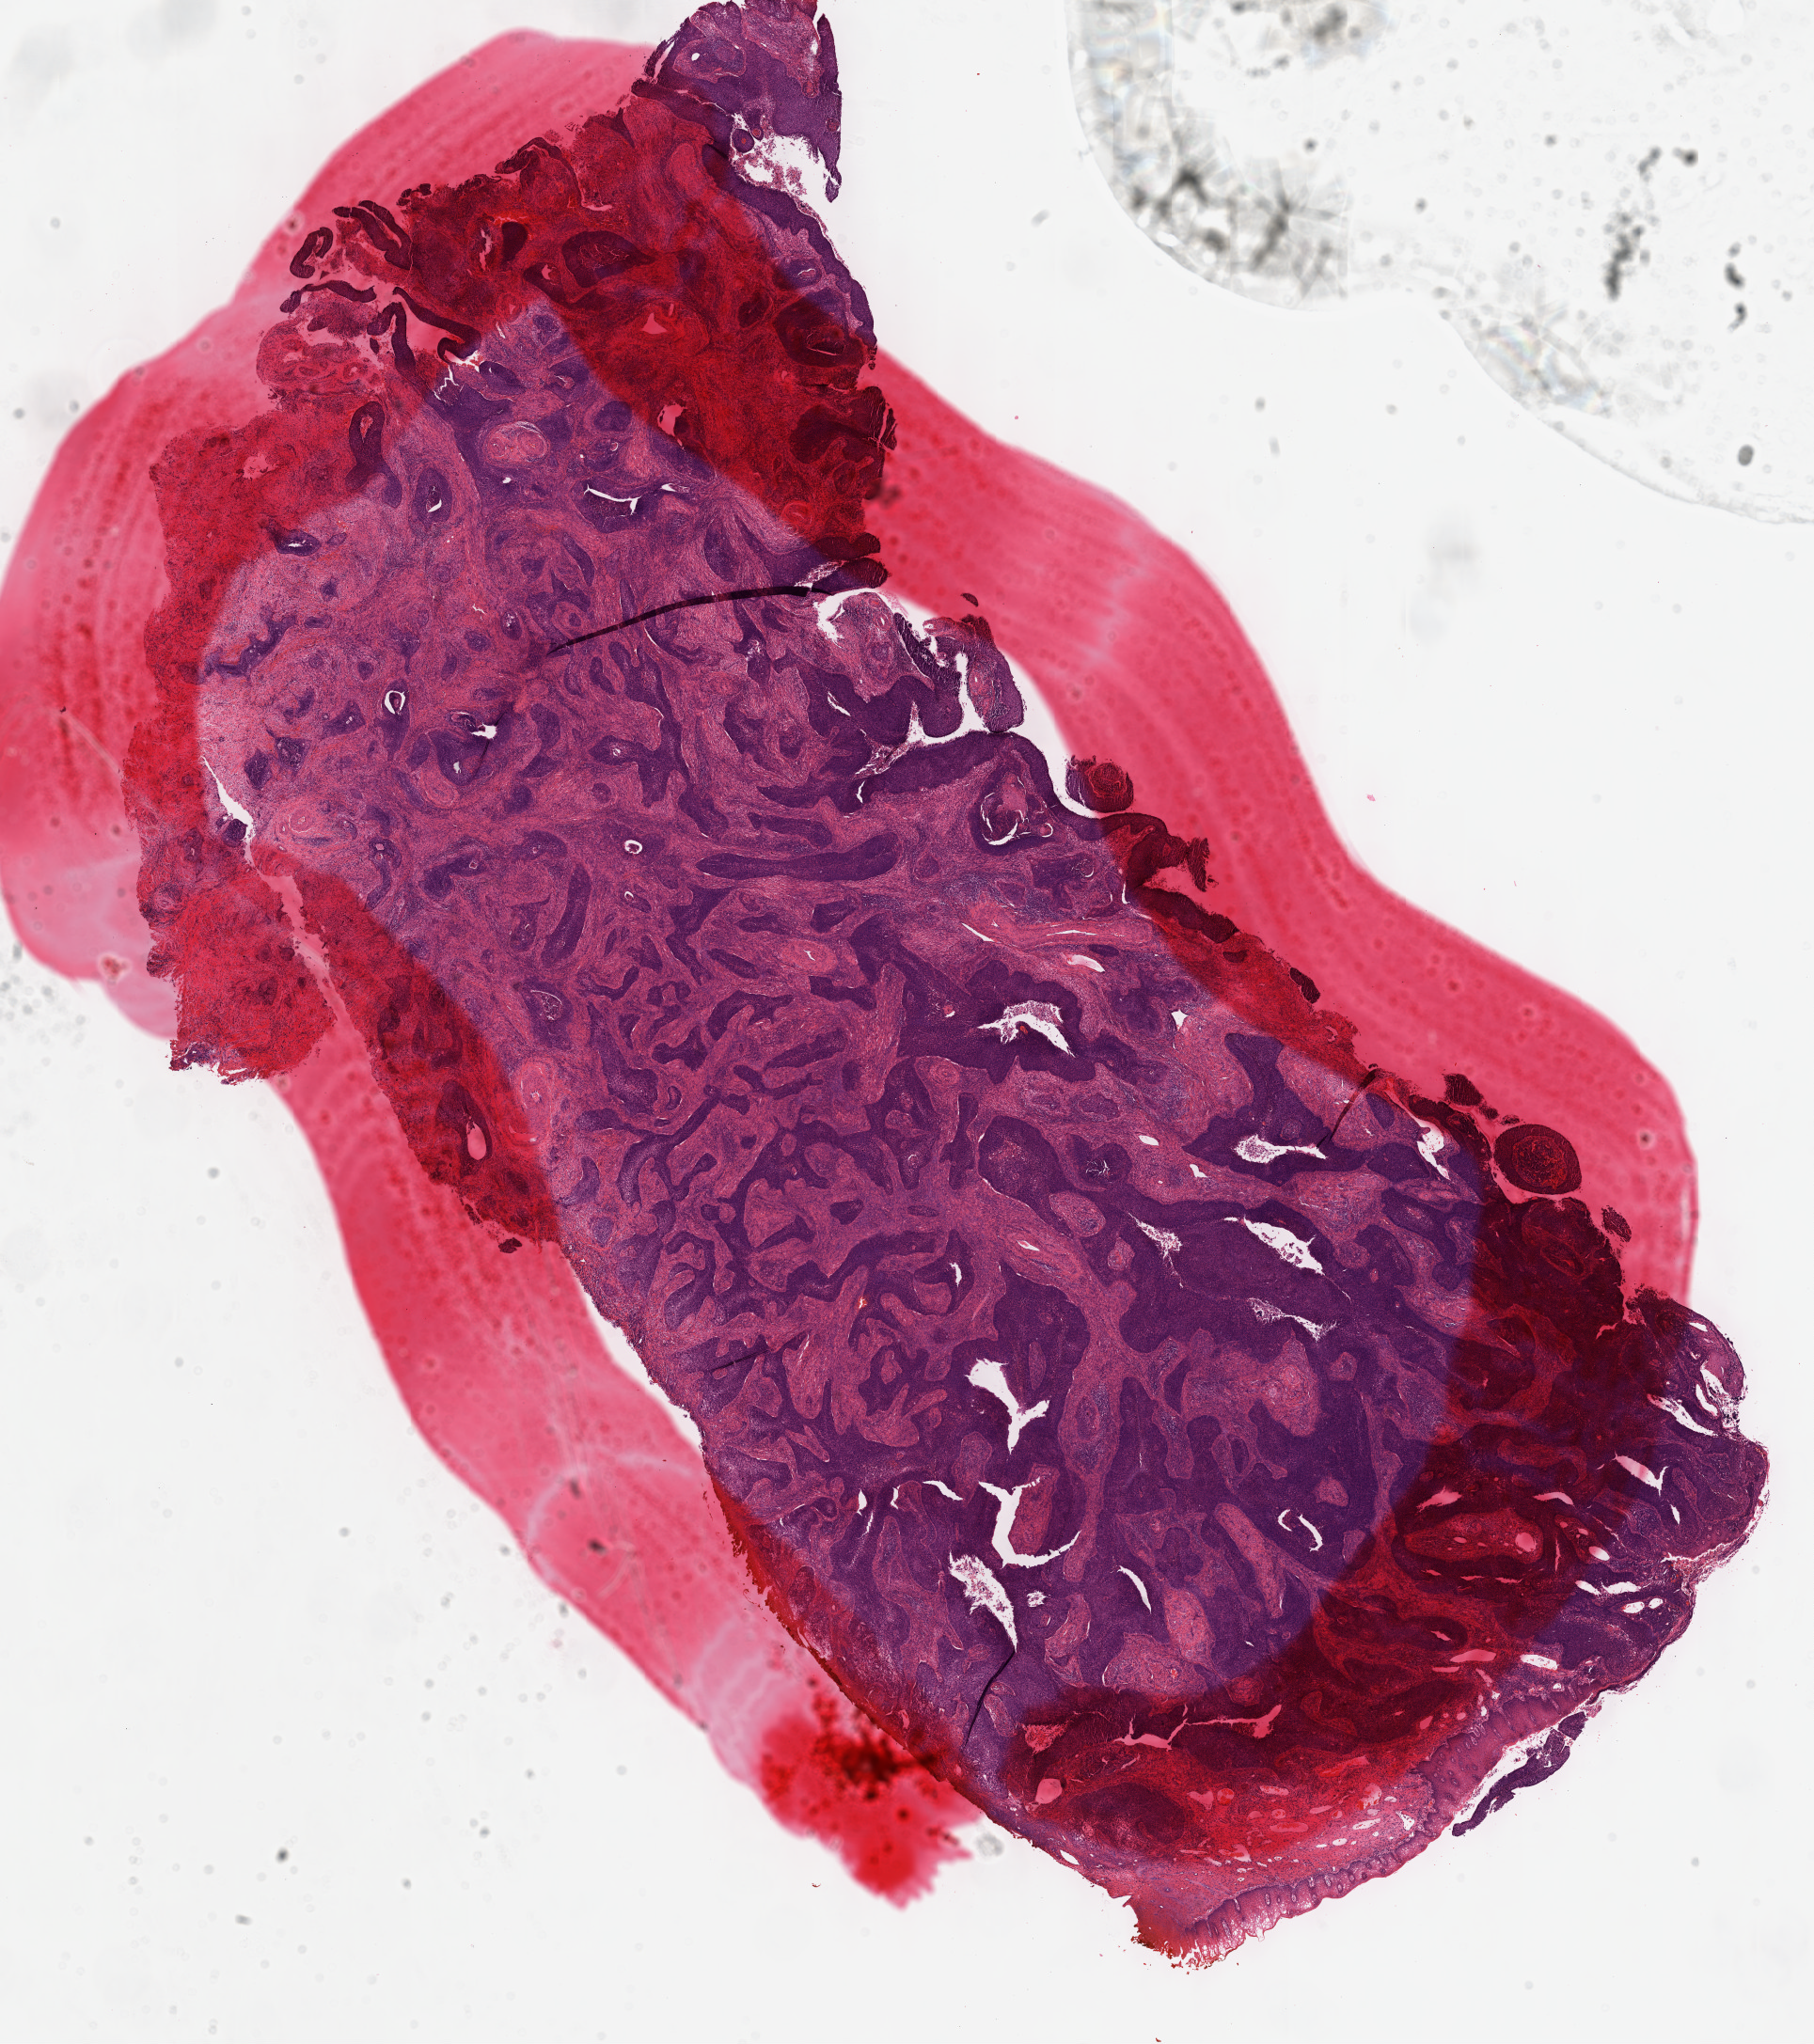
H&E-stained whole-slide image, a low-resolution overview of the entire scanned area, about 15.6 x 17.6 mm, FFPE section, primary tumour sample from the cervix. Female, age 38 years at initial diagnosis.
Diagnosis: Squamous cell carcinoma, NOS (cervix uteri).